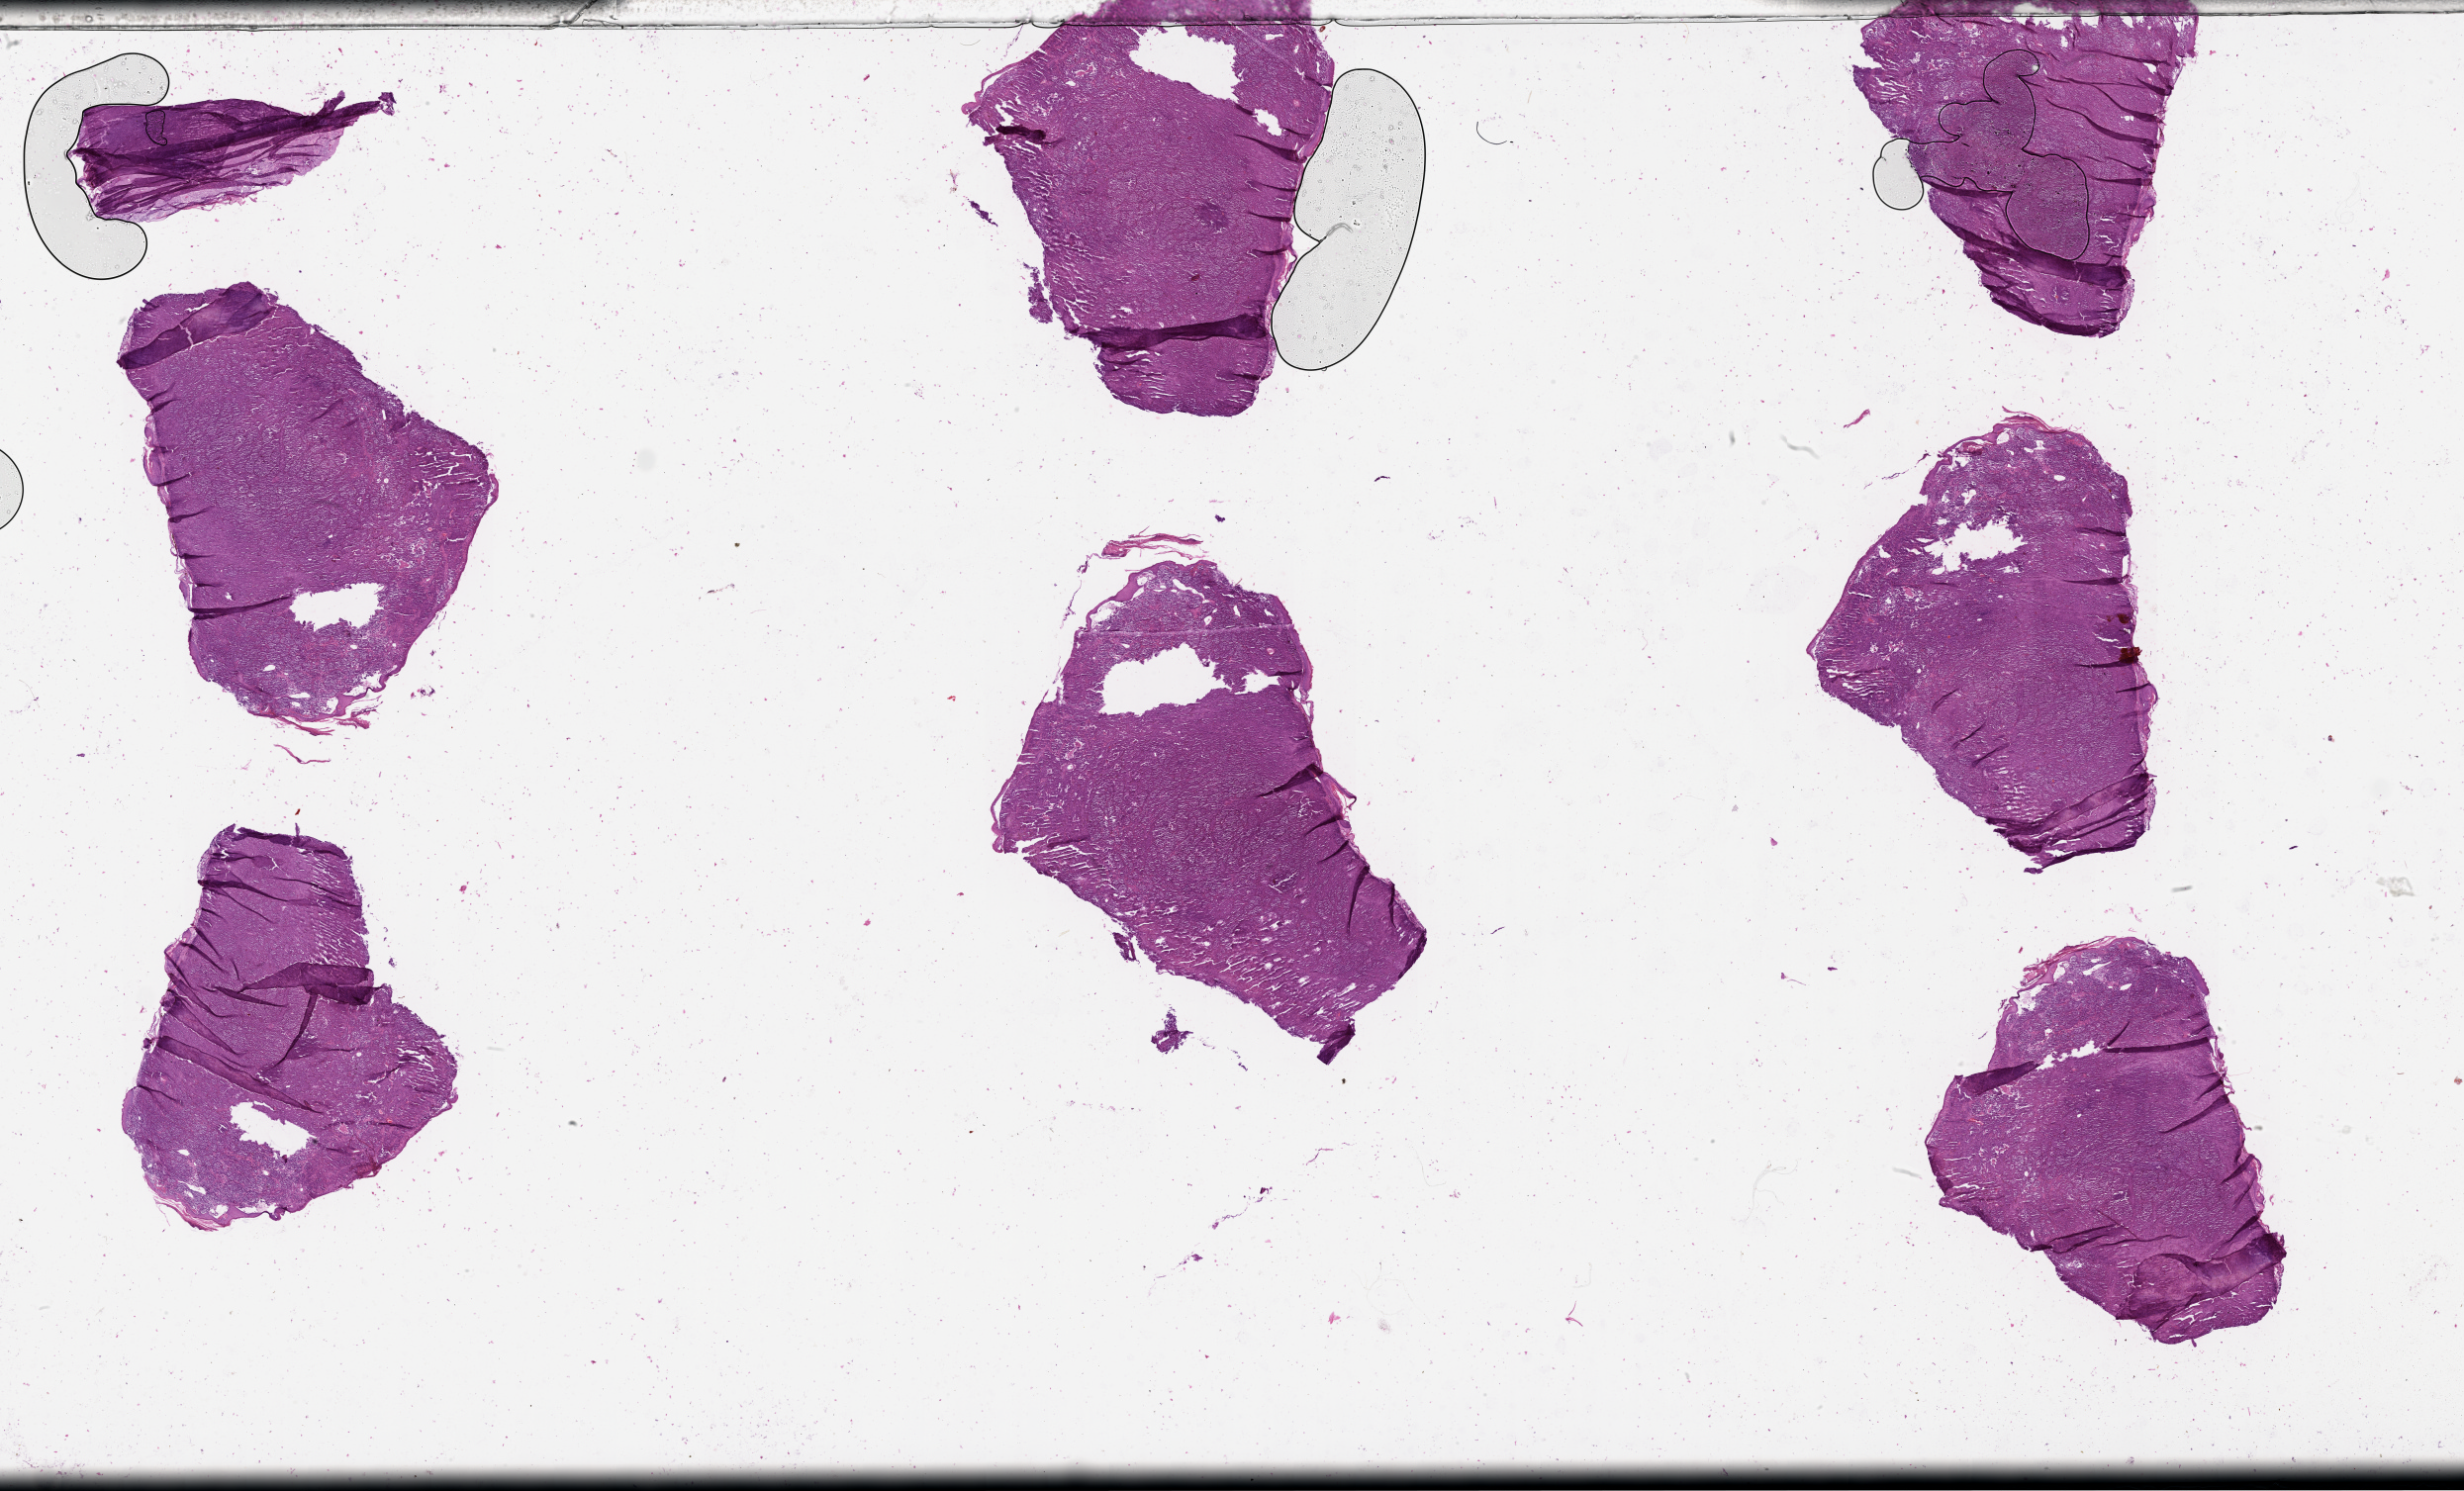
Hematoxylin and eosin (H&E) stained whole-slide image, shown as a low-resolution overview of the whole scanned area (about 40.1 x 24.3 mm, from a 20x scan).
Patient diagnosis (cohort enrolment): cutaneous melanoma (skin).